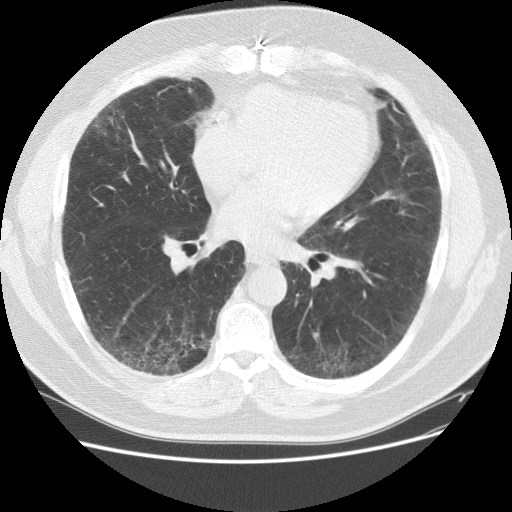
Axial slice from a low-dose chest CT screening exam. Baseline screening round. Lung window (W 1500 / L -600 HU). Slice 75 of 151 in the series. 512 × 512 image matrix. Male participant, aged 59 years at enrolment.
- Lesion marked by an expert reader, bounding box <83,94,132,144> (left, top, right, bottom; pixels).
- The screening reader recorded 2 non-calcified nodules or masses ≥4 mm on this exam (right middle lobe, right lower lobe); which of them this box marks is not recorded.